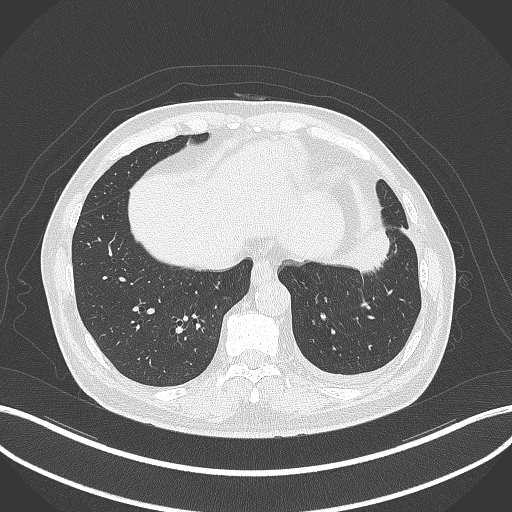
Chest CT, one axial slice; position 88 of 230 along the scan axis; reconstruction kernel B70f; lung window (W 1500 / L -600 HU); 1 mm slice thickness; 512 × 512 image matrix, field of view 400 × 400 mm. Patient: male, 68 years. From the clinical record (not read from this slice): clinical TNM (as recorded): T2b N0 M0.
Annotated regions visible in this slice (bounding box drawn by a radiologist):
- lung tumour (recorded histology: squamous cell carcinoma): bounding box (x1, y1, x2, y2) in pixels: (339, 225, 397, 283)